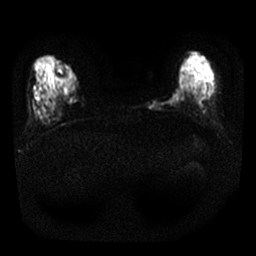
Breast MRI, one axial slice; slice 6 of 24 in the series (ordered by position); diffusion-weighted series; image 2 of 4 stored at this slice position (different b-values; order by instance number); 1.5 T; 4 mm slice thickness; 256 × 256 image matrix, field of view 300 × 300 mm. Female patient.
Structures marked on this image (outlined manually by an expert reader):
- tumour on diffusion-weighted imaging: bounding box (x1, y1, x2, y2) in pixels: (148, 87, 181, 109)